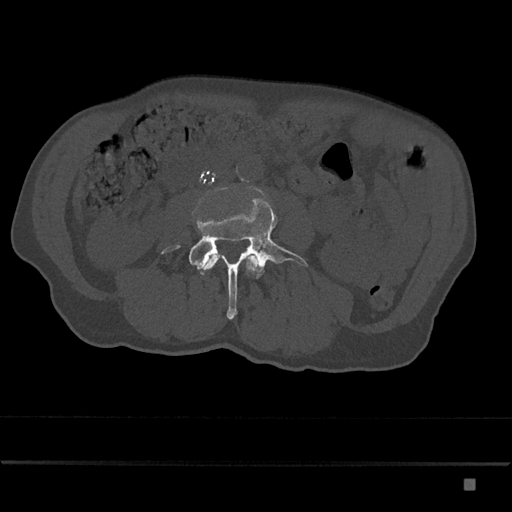
CT including the spine, one axial slice. Slice 356 of 797 in the series (ordered by position). Bone window (W 1800 / L 400 HU). 0.5 mm slice thickness. 512 × 512 image matrix. Patient: male, 72 years. From the clinical record (not read from this slice): primary cancer: prostate.
Outlined on this slice (semi-automatic segmentation, software-assisted and operator-edited):
- L3 vertebra: bounding box <204,255,258,270> (left, top, right, bottom; pixels)
- L4 vertebra: <162,197,308,320>